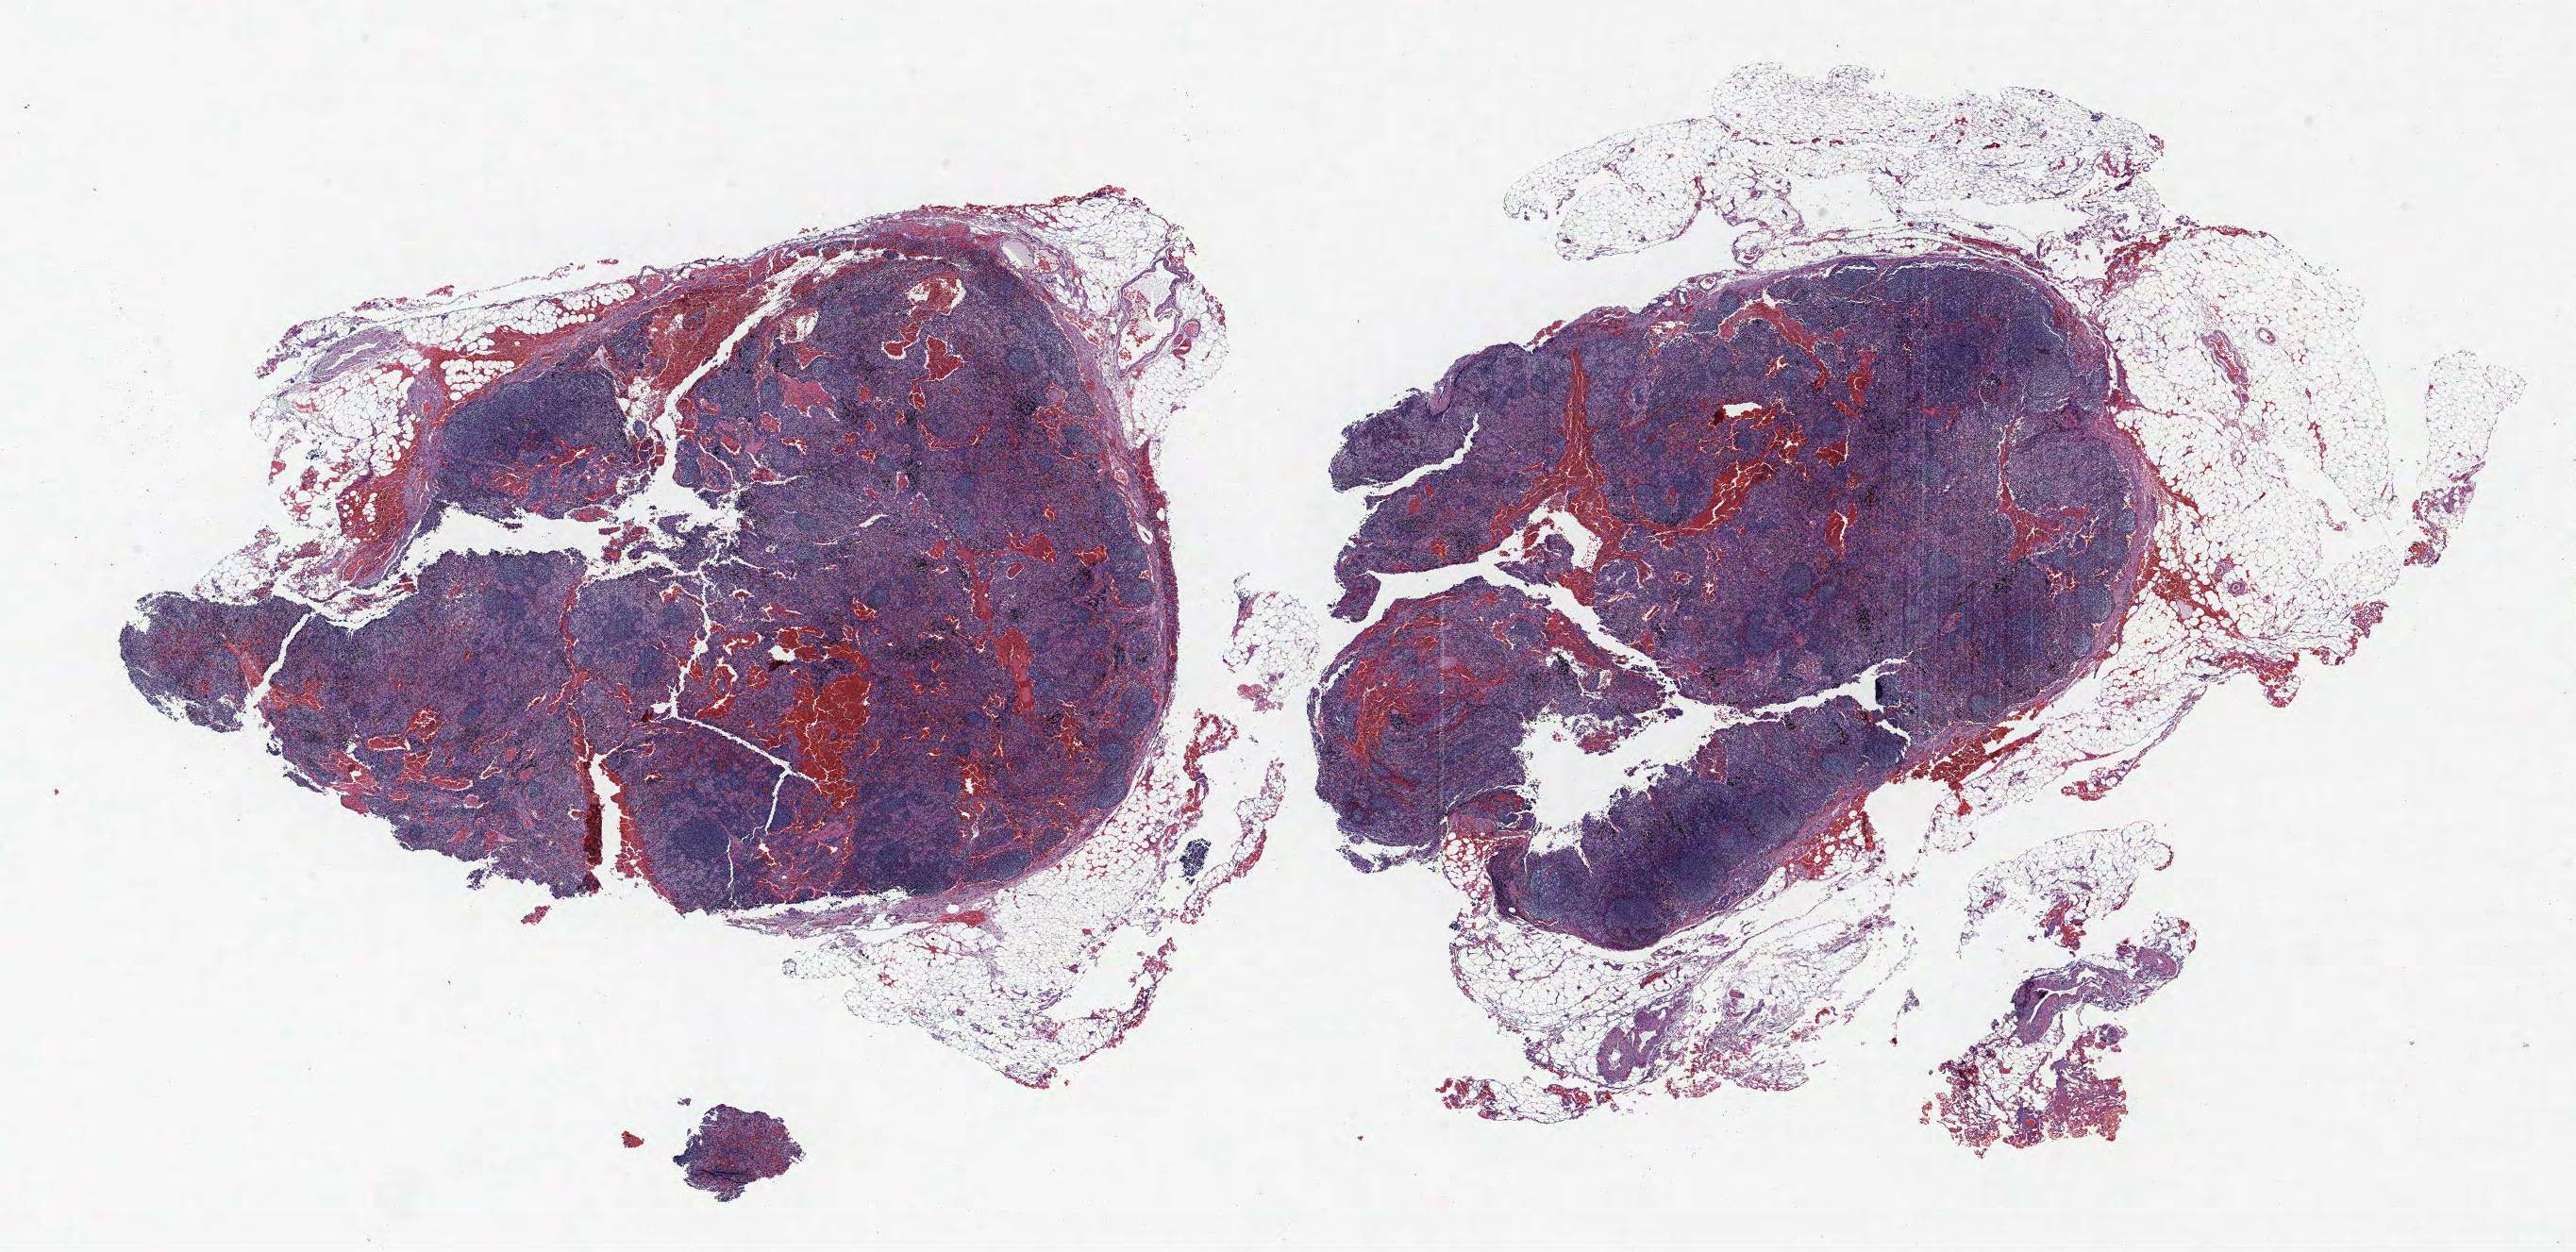
H&E-stained whole-slide image, a low-resolution overview of the entire scanned area, about 21.8 x 10.6 mm, FFPE section, lung tissue. Male patient, aged 65 at enrolment.
Participant's lung-cancer diagnosis: Carcinoma, NOS.